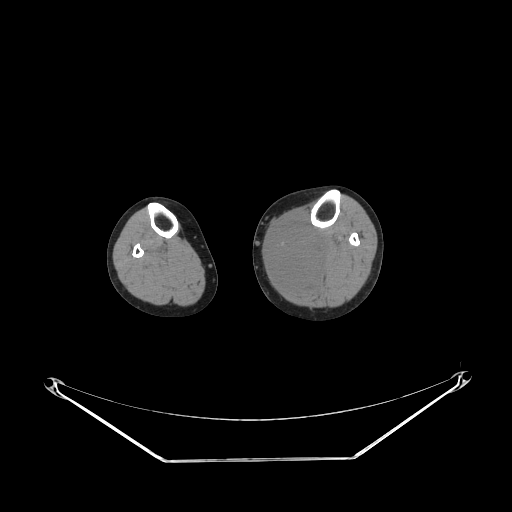
CT of an extremity soft-tissue mass (from a PET/CT study), one axial slice; slice 143 of 223 in the series (ordered by position); reconstruction kernel STANDARD; soft-tissue window (W 400 / L 40 HU); 3.75 mm slice thickness; 512 × 512 image matrix, field of view 500 × 500 mm. Female patient. Case-level facts recorded for this patient, not image findings: histological type: extraskeletal high grade osteogenic sarcoma; grade: high; site of the primary tumour: left calf.
Outlined on this slice (expert contour drawn on MRI and transferred to this co-registered scan by the dataset authors):
- gross tumour volume (mass): bounding box [x1, y1, x2, y2] px = [270, 221, 325, 289]